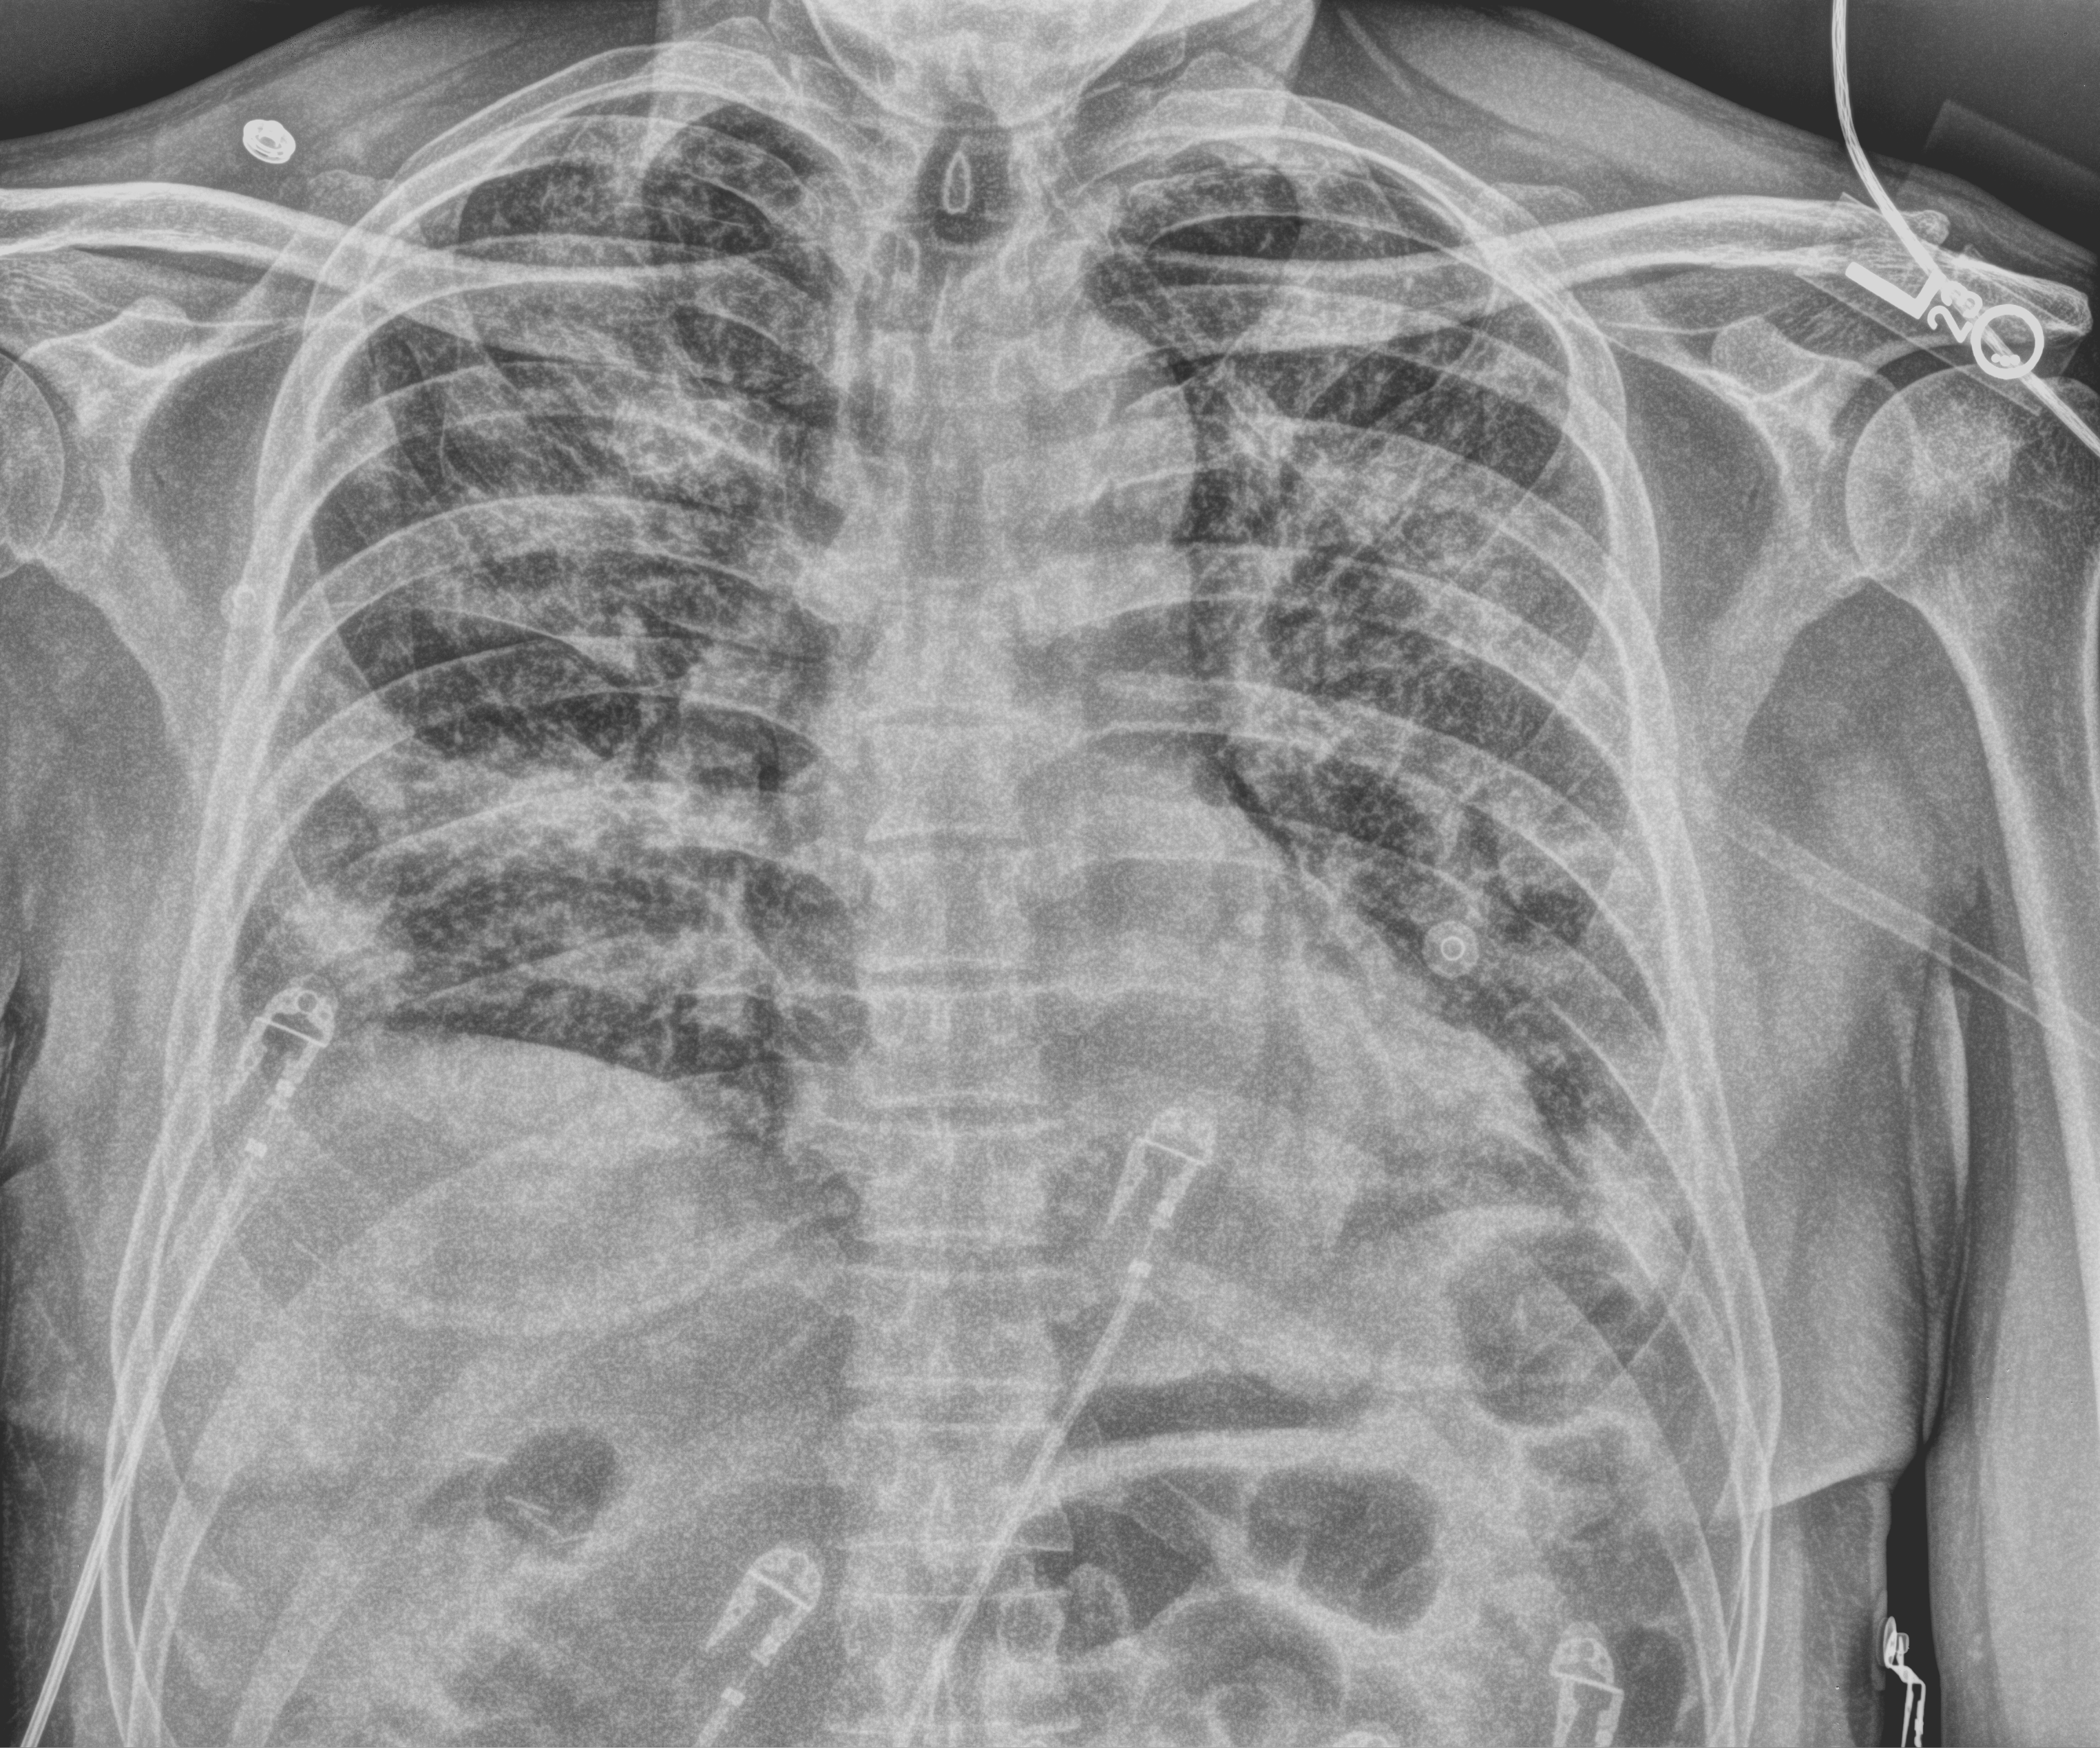
Portable chest radiograph. Patient hospitalised with COVID-19; male, aged 60–74 years.
From the hospital-stay record, not from the radiograph (when in the stay this image was taken is not recorded): admitted to intensive care during this hospital stay: yes.